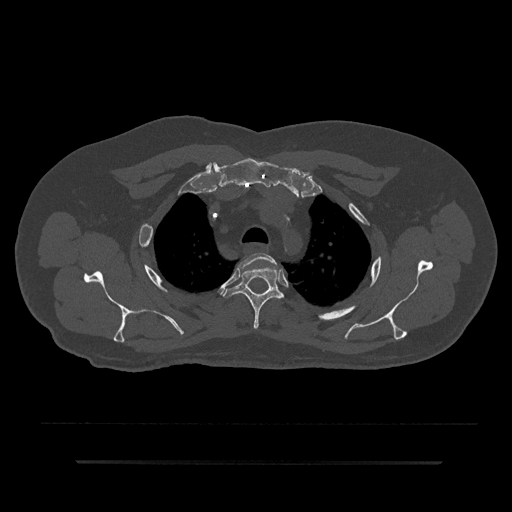
CT including the spine, one axial slice. Position 662 of 797 along the scan axis. Reconstruction kernel Br40s/3. 120 kVp. Bone window (W 1800 / L 400 HU). 0.5 mm slice thickness. 512 × 512 image matrix. Male patient, age 59 years. From the clinical record (not read from this slice): primary cancer: bile ducts; vertebrae with lytic lesions (as recorded): T10.
Annotated regions visible in this slice (semi-automatically segmented with operator editing):
- T2 vertebra: bounding box <236,252,277,269> (left, top, right, bottom; pixels)
- T3 vertebra: <224,267,284,329>